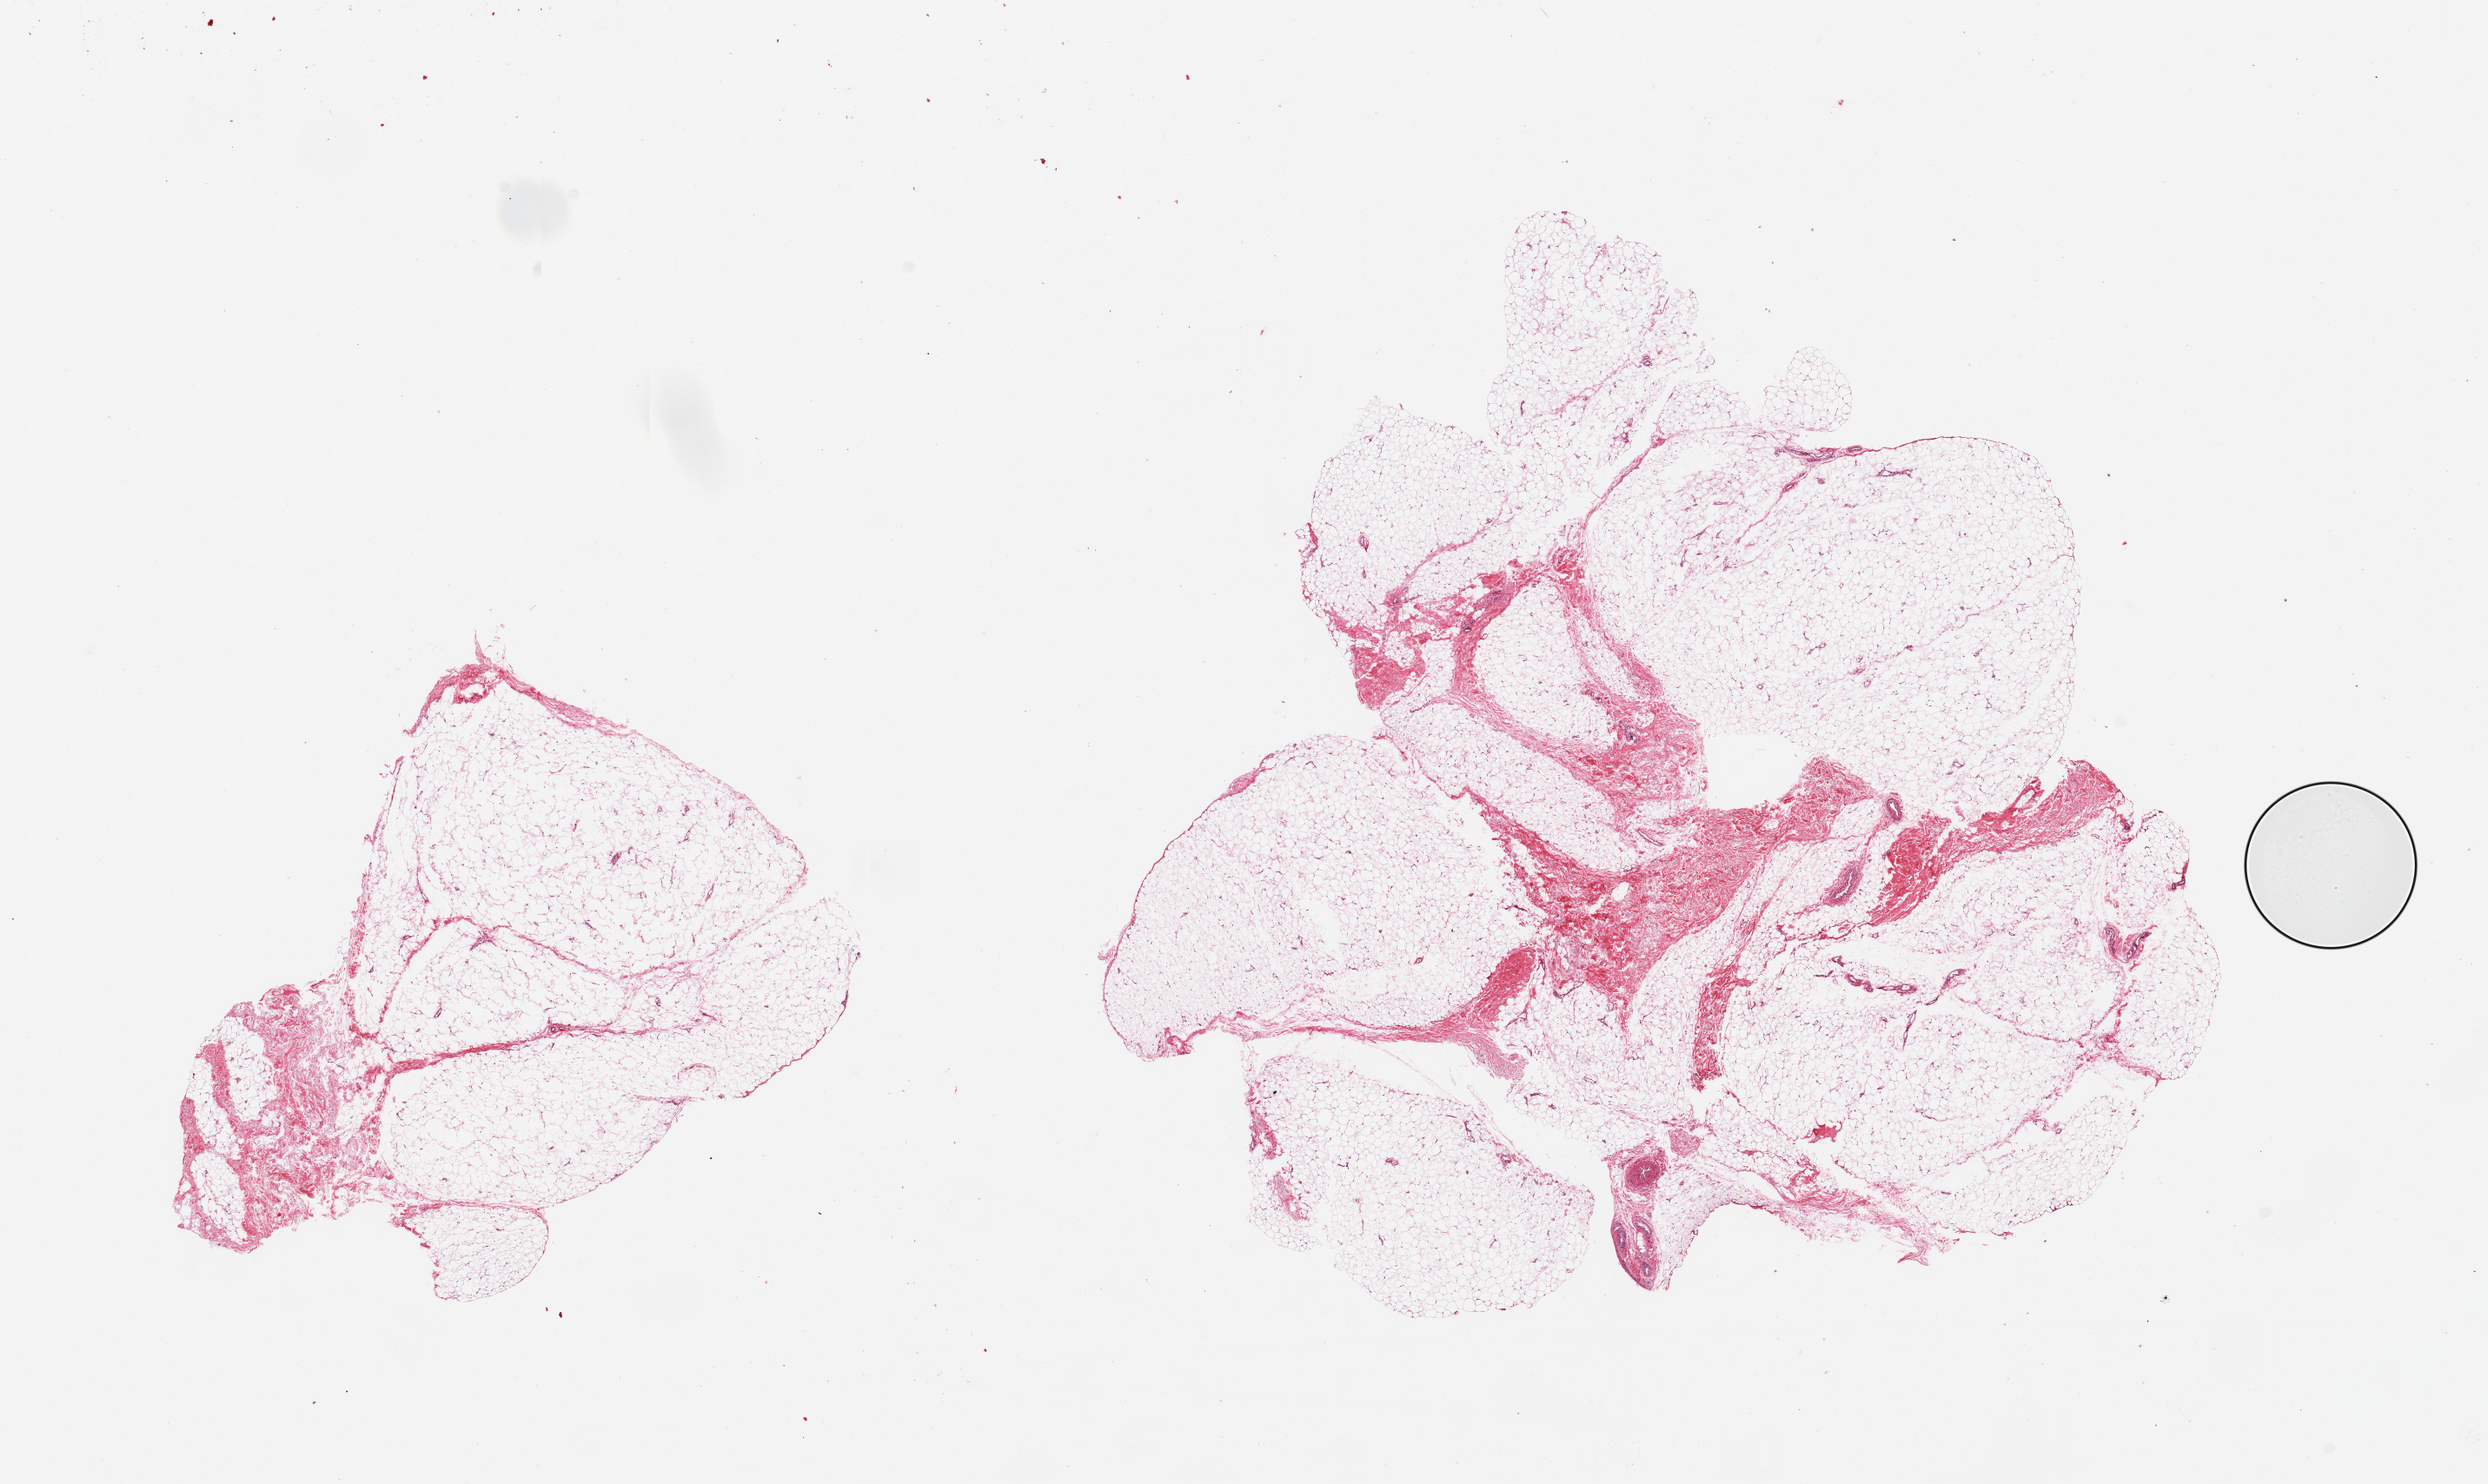
Whole-slide image, haematoxylin and eosin stain, a low-resolution overview of the entire scanned area, about 22.6 x 13.5 mm (acquisition: 20x scan). PAXgene-fixed paraffin-embedded (PFPE) section. Sampled site (target tissue): adipose tissue. Tissue donor sample. Male donor.
* review note (as recorded): 2 pieces, fascia/vascular elements are ~20% of tissue